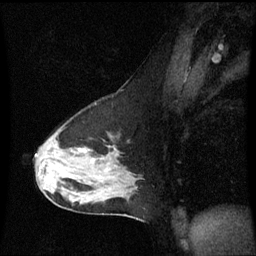
Breast MRI (dynamic contrast-enhanced), one sagittal slice; position 39 of 60 along the scan axis; dynamic contrast-enhanced series, image 2 of 3 at this slice position (ordered by acquisition); 1.5 T; TE 4.2 ms, TR 8.9 ms; 256 × 256 image matrix, field of view 210 × 210 mm. Patient: female, 50 years. Case-level facts recorded for this patient, not image findings: setting: breast cancer imaged before/during neoadjuvant chemotherapy; receptor status: HR-positive, HER2-negative.
Structures marked on this image (semi-automatically segmented with operator editing):
- analysis volume of interest (the breast-tissue region the enhancement analysis was run in; not a lesion): bounding box (x1, y1, x2, y2) in pixels: (34, 126, 142, 210)
- tumour enhancement mask (voxels above the 70 % enhancement threshold inside the analysis volume of interest): (81, 150, 86, 153)